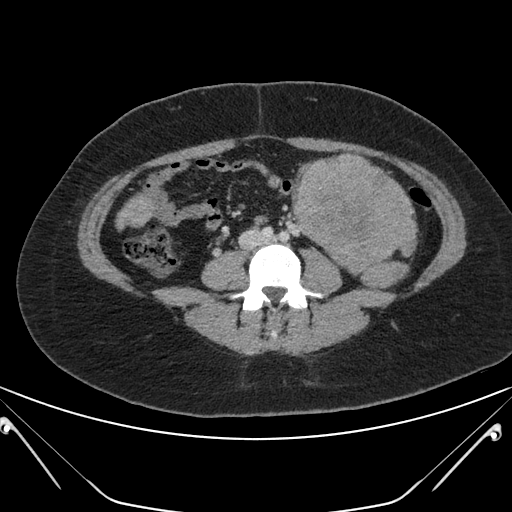
Contrast-enhanced abdominal CT, one axial slice; slice 81 of 168 in the series (ordered by position); soft-tissue window (W 400 / L 40 HU); 3 mm slice thickness; 512 × 512 image matrix. Female patient, age 26 years. From the clinical record (not read from this slice): diagnosis: adrenocortical carcinoma; tumour side: left adrenal; tumour size at pathology: 28 cm; Ki-67 index: 20 %; stage (as recorded): 2.
Structures marked on this image (semi-automatic segmentation, software-assisted and operator-edited):
- mass: bounding box [x1, y1, x2, y2] px = [293, 154, 416, 287]